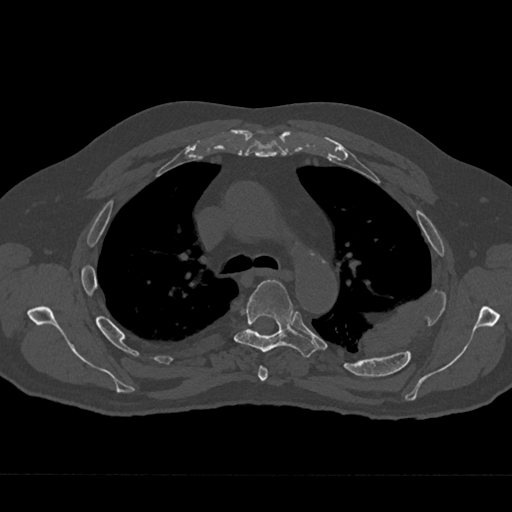
CT including the spine, one axial slice; slice 480 of 797 in the series (ordered by position); reconstruction kernel Br40s/3; bone window (W 1800 / L 400 HU); 0.5 mm slice thickness; 512 × 512 image matrix, field of view 377 × 377 mm. Male patient, age 75 years. From the clinical record (not read from this slice): primary cancer: renal; vertebrae with lytic lesions (as recorded): T4.
Outlined on this slice (semi-automatic segmentation, software-assisted and operator-edited):
- T4 vertebra: bounding box (x1, y1, x2, y2) in pixels: (258, 365, 268, 381)
- T5 vertebra: (234, 279, 317, 357)